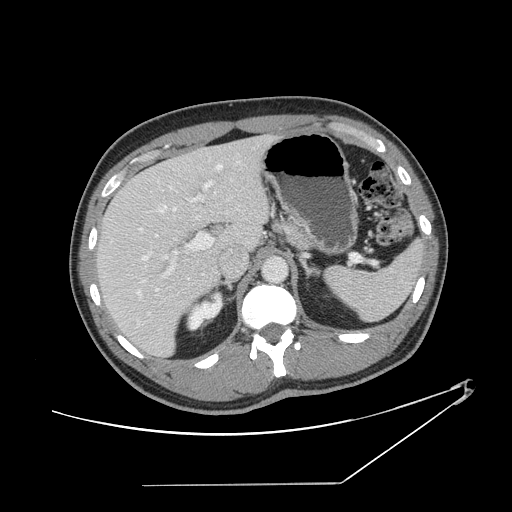
Contrast-enhanced abdominal CT, one axial slice; position 91 of 152 along the scan axis; intravenous contrast given; soft-tissue window (W 400 / L 40 HU); 2.5 mm slice thickness; 512 × 512 image matrix. Male patient, age 45 years. Case-level facts recorded for this patient, not image findings: diagnosis: colorectal cancer liver metastases, imaged before liver resection; multiple liver metastases: no; largest metastasis: 1 cm; chemotherapy before resection: yes.
Outlined on this slice (manually delineated by an expert):
- hepatic veins: box from (x=111, y=163) to (x=238, y=297) px
- liver: (x=98, y=137)–(x=269, y=355)
- planned liver remnant (the part of the liver to remain after resection): (x=98, y=155)–(x=226, y=355)
- portal vein (with intrahepatic branches): (x=139, y=181)–(x=214, y=315)